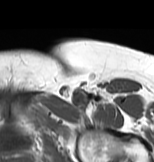
MRI of an extremity soft-tissue mass, one axial slice. Slice 59 of 83 in the series (ordered by position). MR volume resampled by the dataset authors to the PET/CT grid (not the native acquisition matrix). 3.27 mm slice thickness. 154 × 162 image matrix, field of view 150 × 158 mm. Female patient. From the clinical record (not read from this slice): histological type: myxofibrosarcoma; grade: intermediate; site of the primary tumour: left thigh.
Annotated regions visible in this slice (expert contour drawn on MRI and transferred to this co-registered scan by the dataset authors):
- gross tumour volume including surrounding oedema: bounding box <60,91,111,113> (left, top, right, bottom; pixels)